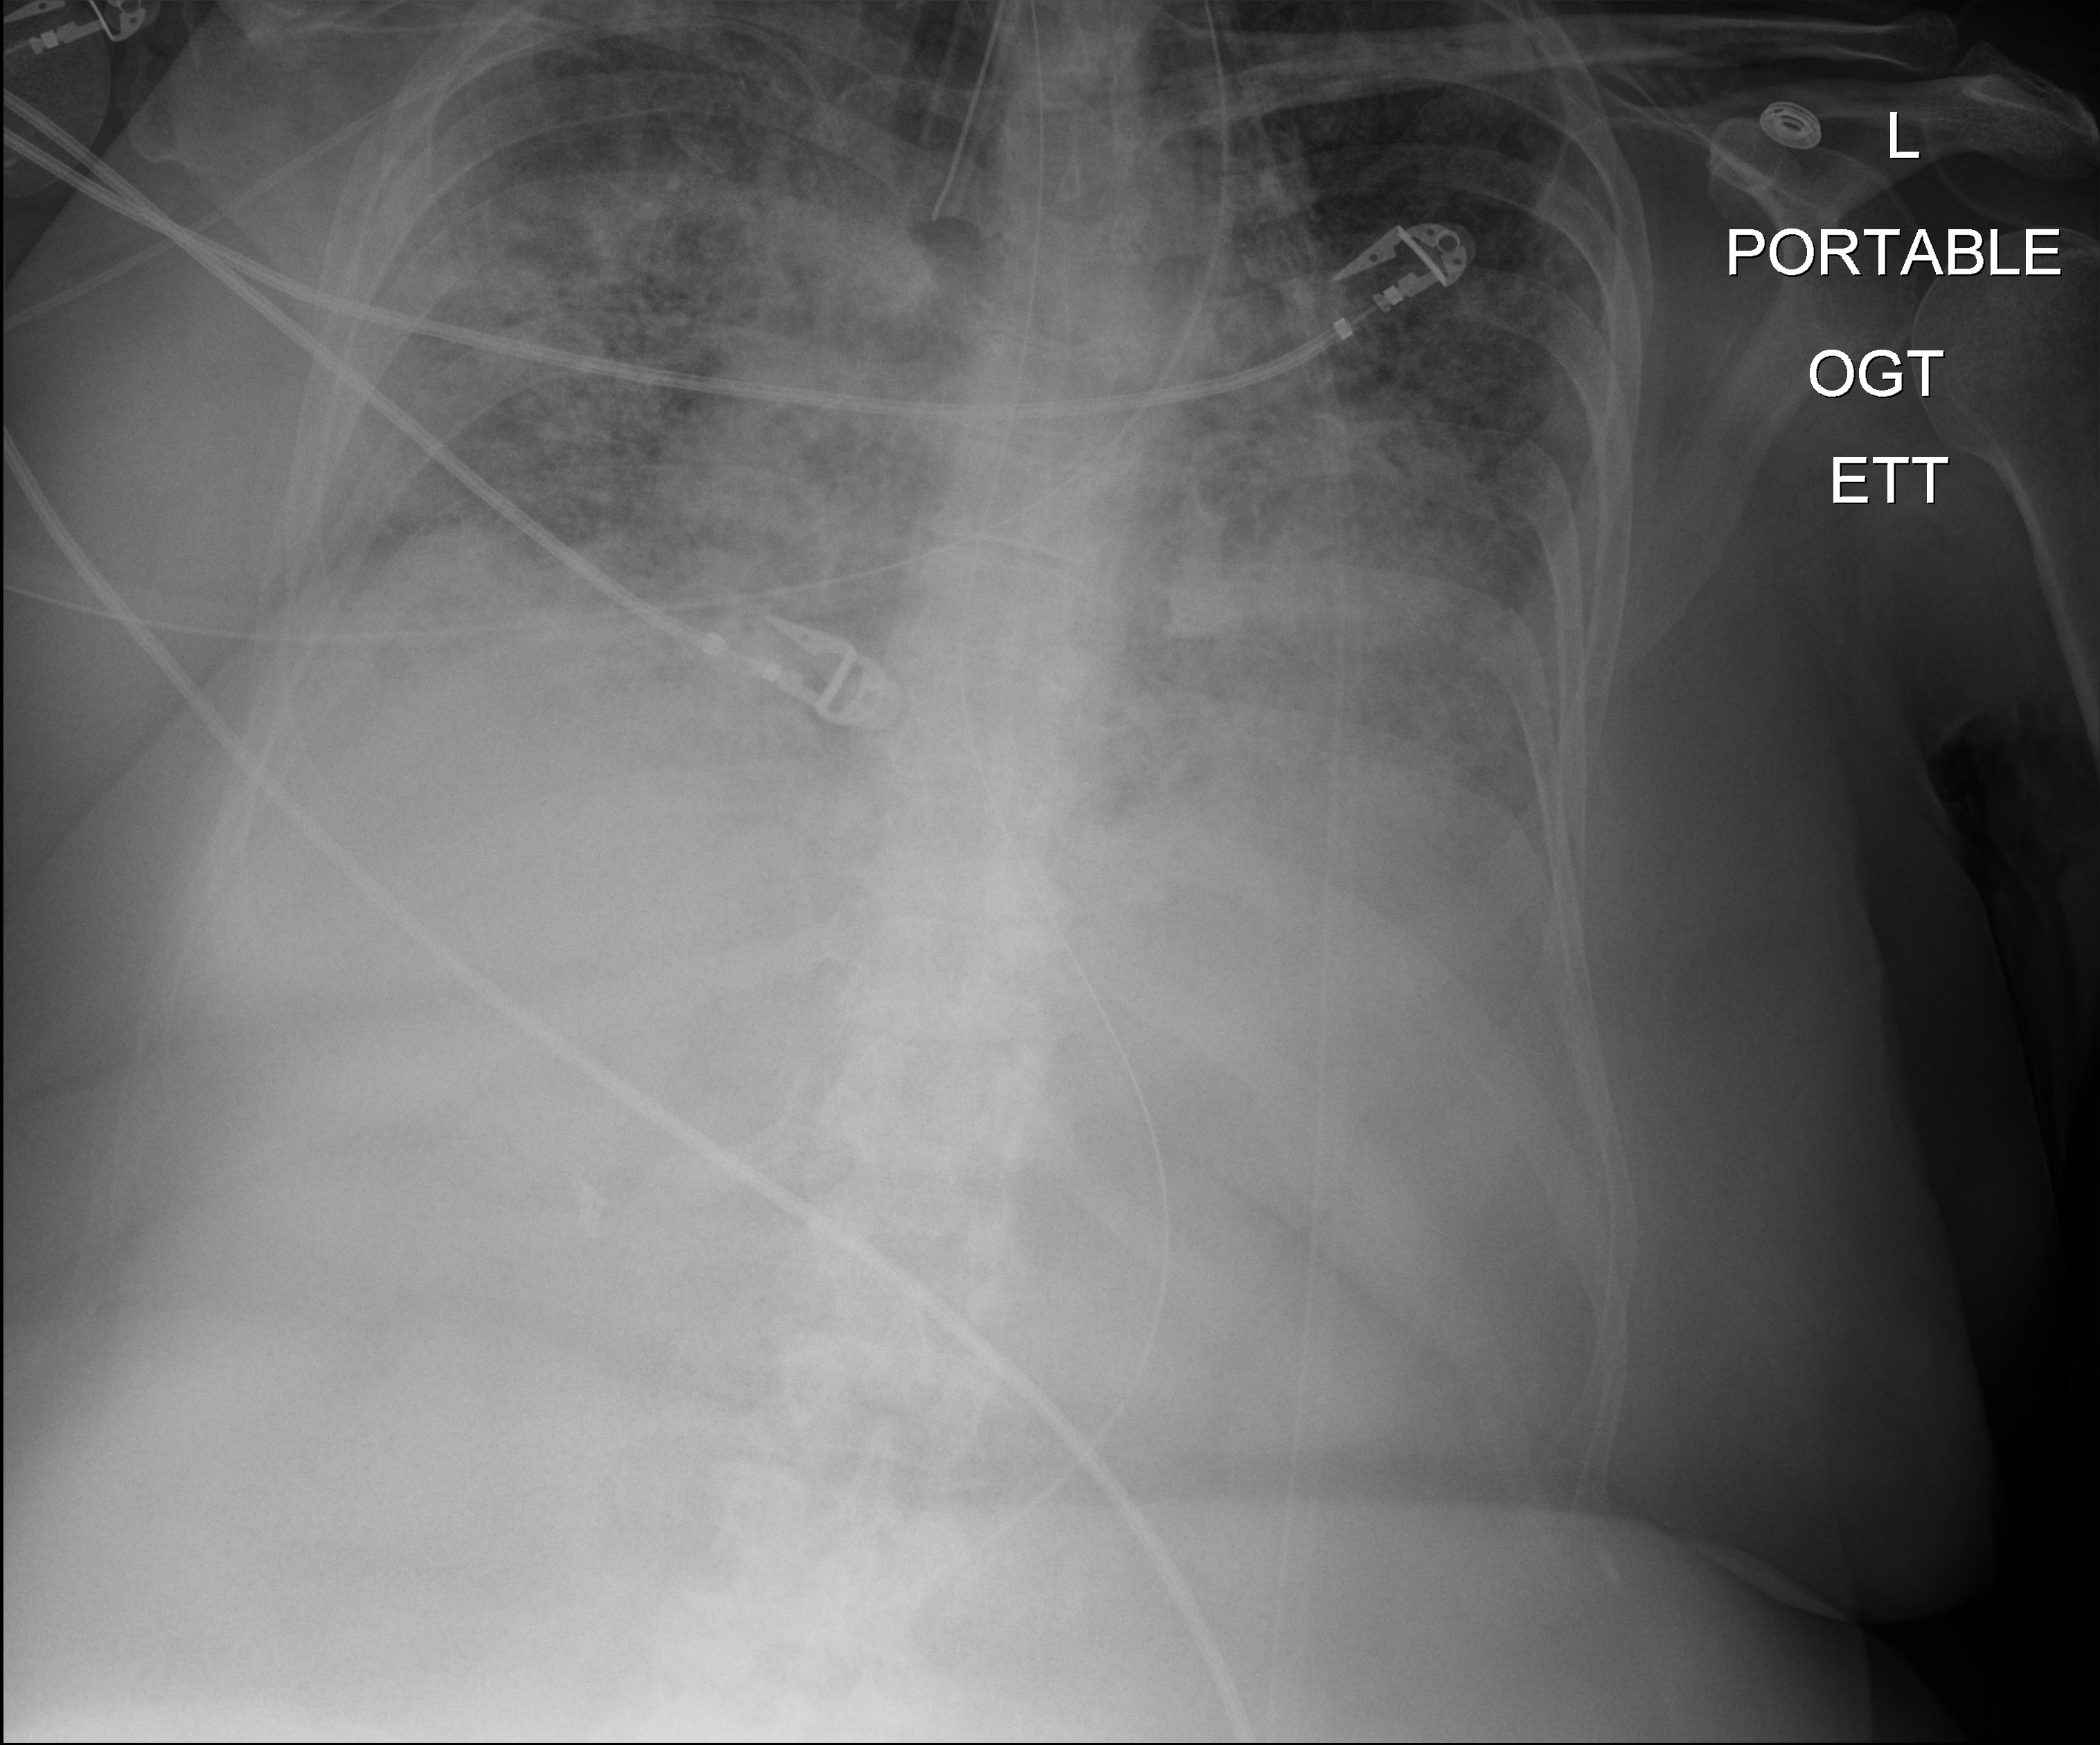
Bedside chest radiograph (digital radiography), anteroposterior (AP) projection. Female patient hospitalised with COVID-19, age 60–74 years.
From the hospital-stay record, not from the radiograph (when in the stay this image was taken is not recorded): admitted to intensive care during this hospital stay: yes; length of hospital stay: 45 days.